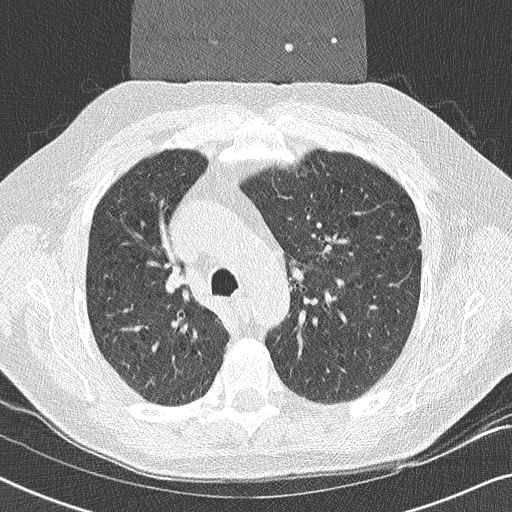
Low-dose screening chest CT, one axial slice. Reconstruction kernel B50f. Lung window (W 1500 / L -600 HU). 2 mm slice thickness. 512 × 512 image matrix.
Structures marked on this image (expert manual segmentation):
- lesion 1 (tumor, upper lobe of right lung): bounding box [x1, y1, x2, y2] px = [166, 271, 184, 292]